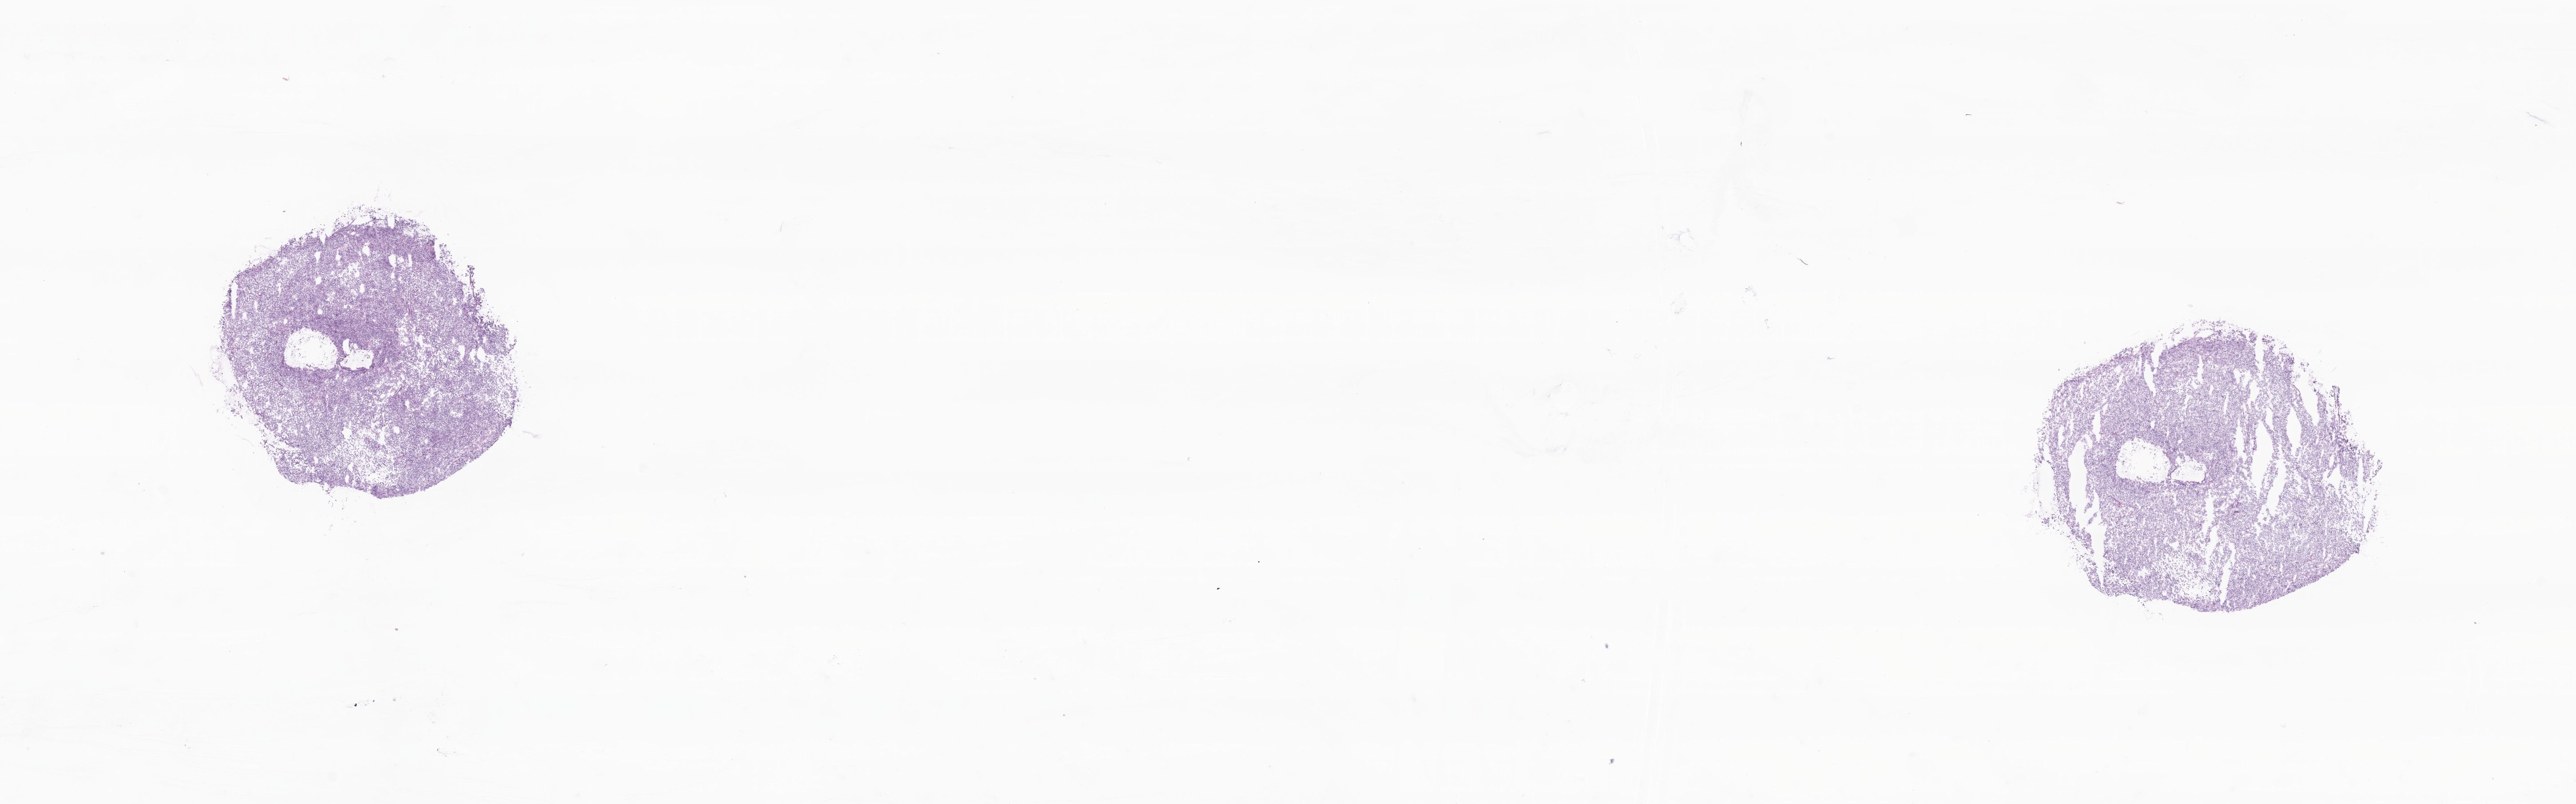
Digitized H&E-stained section of tumor tissue from the upper limb, shown as a low-resolution overview of the whole scanned area (about 24.5 x 7.6 mm). Frozen section (OCT-embedded). Patient male; age 113 months (9 years 5 months).
Diagnosis: Epithelioid sarcoma, NOS.